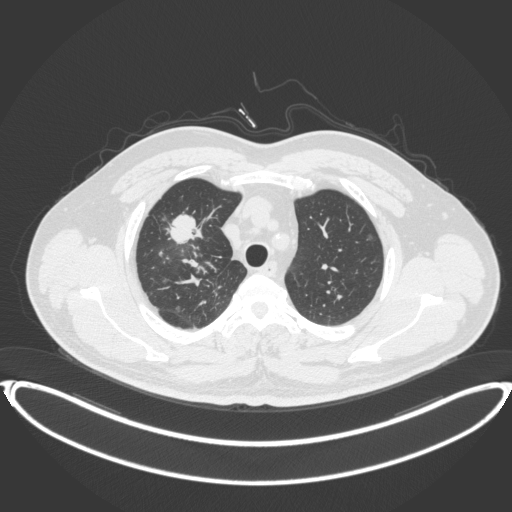
Chest CT, one axial slice; lung window (W 1500 / L -600 HU); 1 mm slice thickness; 512 × 512 image matrix, field of view 445 × 445 mm. Male patient, age 53 years. Case-level facts recorded for this patient, not image findings: clinical TNM (as recorded): T2a N0 M0.
Annotated regions visible in this slice (bounding box drawn by a radiologist):
- lung tumour (recorded histology: adenocarcinoma): bounding box [x1, y1, x2, y2] px = [165, 211, 210, 247]